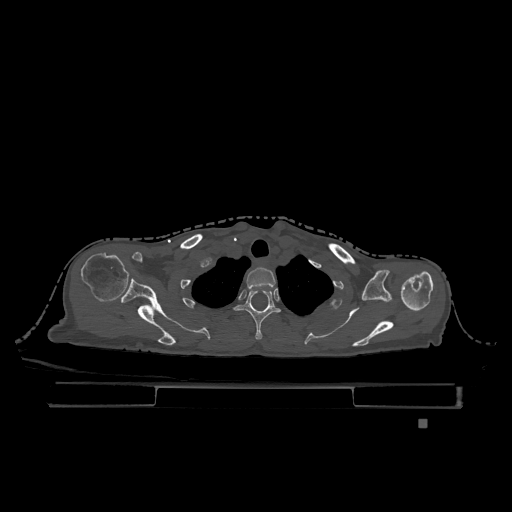
CT including the spine, one axial slice. Position 968 of 1317 along the scan axis. Bone window (W 1800 / L 400 HU). 0.5 mm slice thickness. 512 × 512 image matrix, field of view 500 × 500 mm. Patient: female, 74 years. From the clinical record (not read from this slice): primary cancer: lung.
Outlined on this slice (semi-automatically segmented with operator editing):
- T1 vertebra: box from (x=246, y=267) to (x=276, y=289) px
- T2 vertebra: (x=234, y=290)–(x=281, y=340)